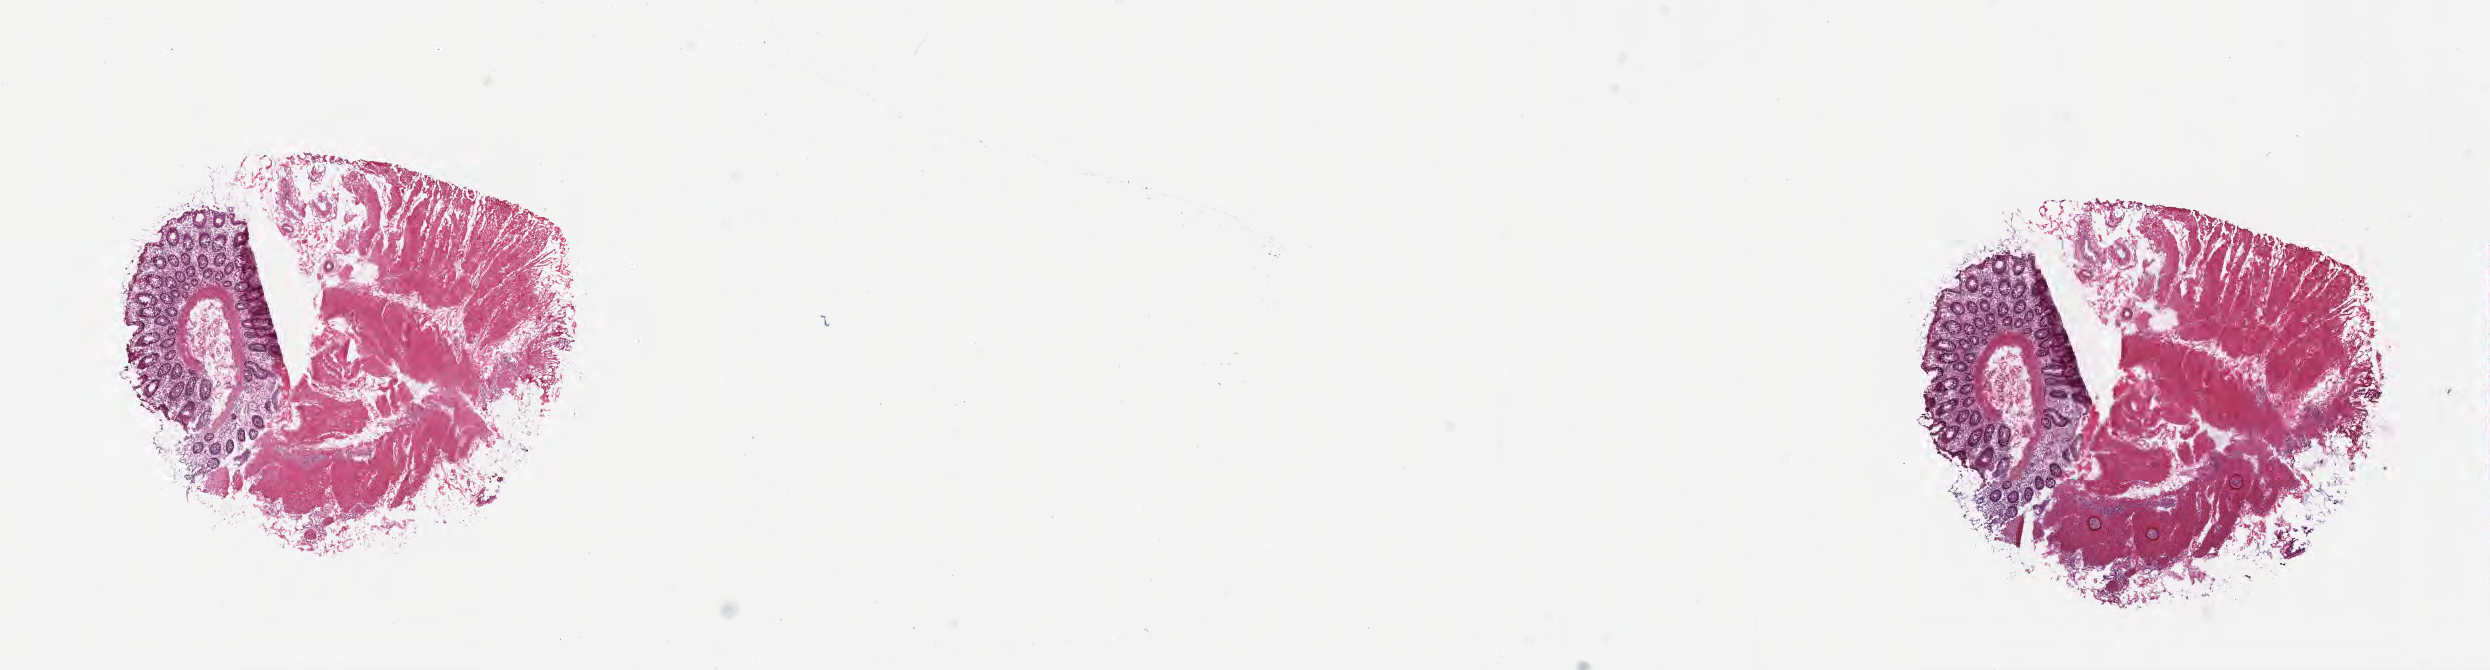
Digitized H&E-stained section — low-resolution overview of the scanned area, about 20.1 x 5.4 mm; cryosection; specimen: normal-tissue sample (non-tumor) from a patient with adenocarcinoma, NOS; site: cecum. Male, age 74 years at initial diagnosis.
This section: non-tumor tissue sample; the patient's diagnosis is given above.